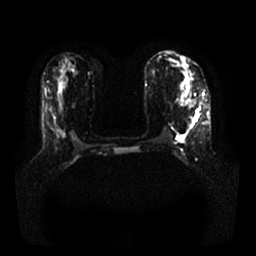
Breast MRI, one axial slice; diffusion-weighted series; image 2 of 4 stored at this slice position (different b-values; order by instance number); 1.5 T; 4 mm slice thickness; 256 × 256 image matrix. Female patient.
Annotated regions visible in this slice (expert manual segmentation):
- tumour on diffusion-weighted imaging: box from (x=193, y=109) to (x=199, y=121) px